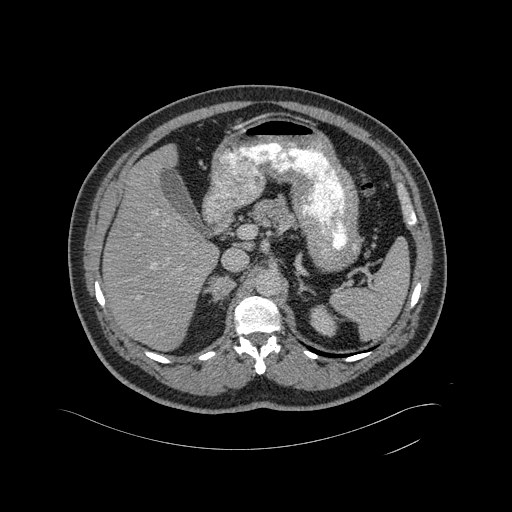
Contrast-enhanced abdominal CT, one axial slice. Position 317 of 433 along the scan axis. Intravenous contrast given. Soft-tissue window (W 400 / L 40 HU). 2 mm slice thickness. 512 × 512 image matrix, field of view 500 × 500 mm. Male patient, age 56 years. From the clinical record (not read from this slice): diagnosis: adrenocortical carcinoma; tumour side: right adrenal; tumour size at pathology: 11.6 cm; Ki-67 index: 50 %; stage (as recorded): 3.
Structures marked on this image (semi-automatically segmented with operator editing):
- mass: bounding box [x1, y1, x2, y2] px = [212, 278, 234, 299]